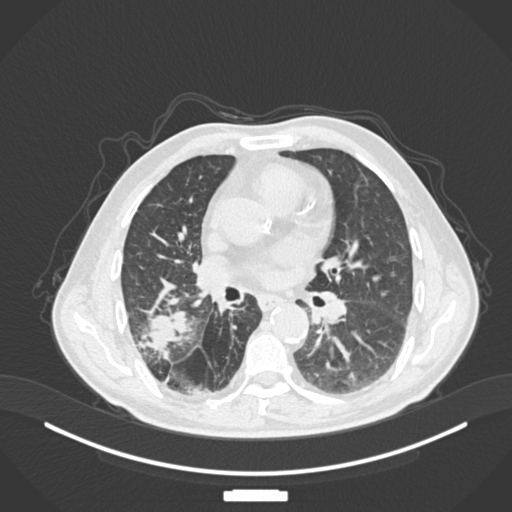
Chest CT, one axial slice. Slice 84 of 201 in the series (ordered by position). Reconstruction kernel B30f. 120 kVp. Lung window (W 1500 / L -600 HU). 1 mm slice thickness. 512 × 512 image matrix, field of view 400 × 400 mm. Patient: male, 72 years. From the clinical record (not read from this slice): clinical TNM (as recorded): T3 N2 M0.
Structures marked on this image (bounding box drawn by a radiologist):
- lung tumour (recorded histology: adenocarcinoma): bounding box (x1, y1, x2, y2) in pixels: (141, 310, 191, 350)